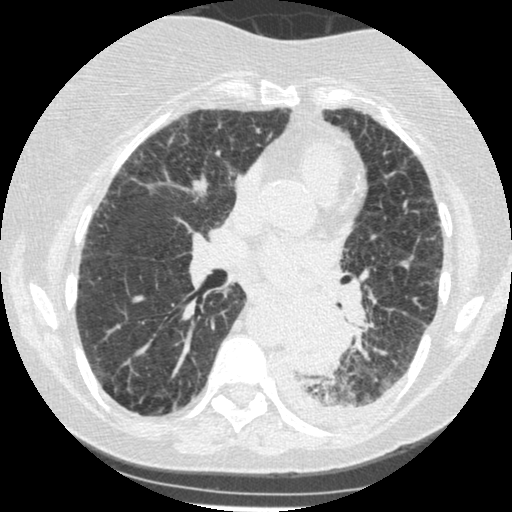
Low-dose screening chest CT, one axial slice. Slice 127 of 341 in the series (ordered by position). Reconstruction kernel STANDARD. Lung window (W 1500 / L -600 HU). 1.25 mm slice thickness. 512 × 512 image matrix.
Outlined on this slice (expert manual segmentation):
- lesion 1 (tumor, lower lobe of left lung): bounding box [x1, y1, x2, y2] px = [284, 303, 347, 375]